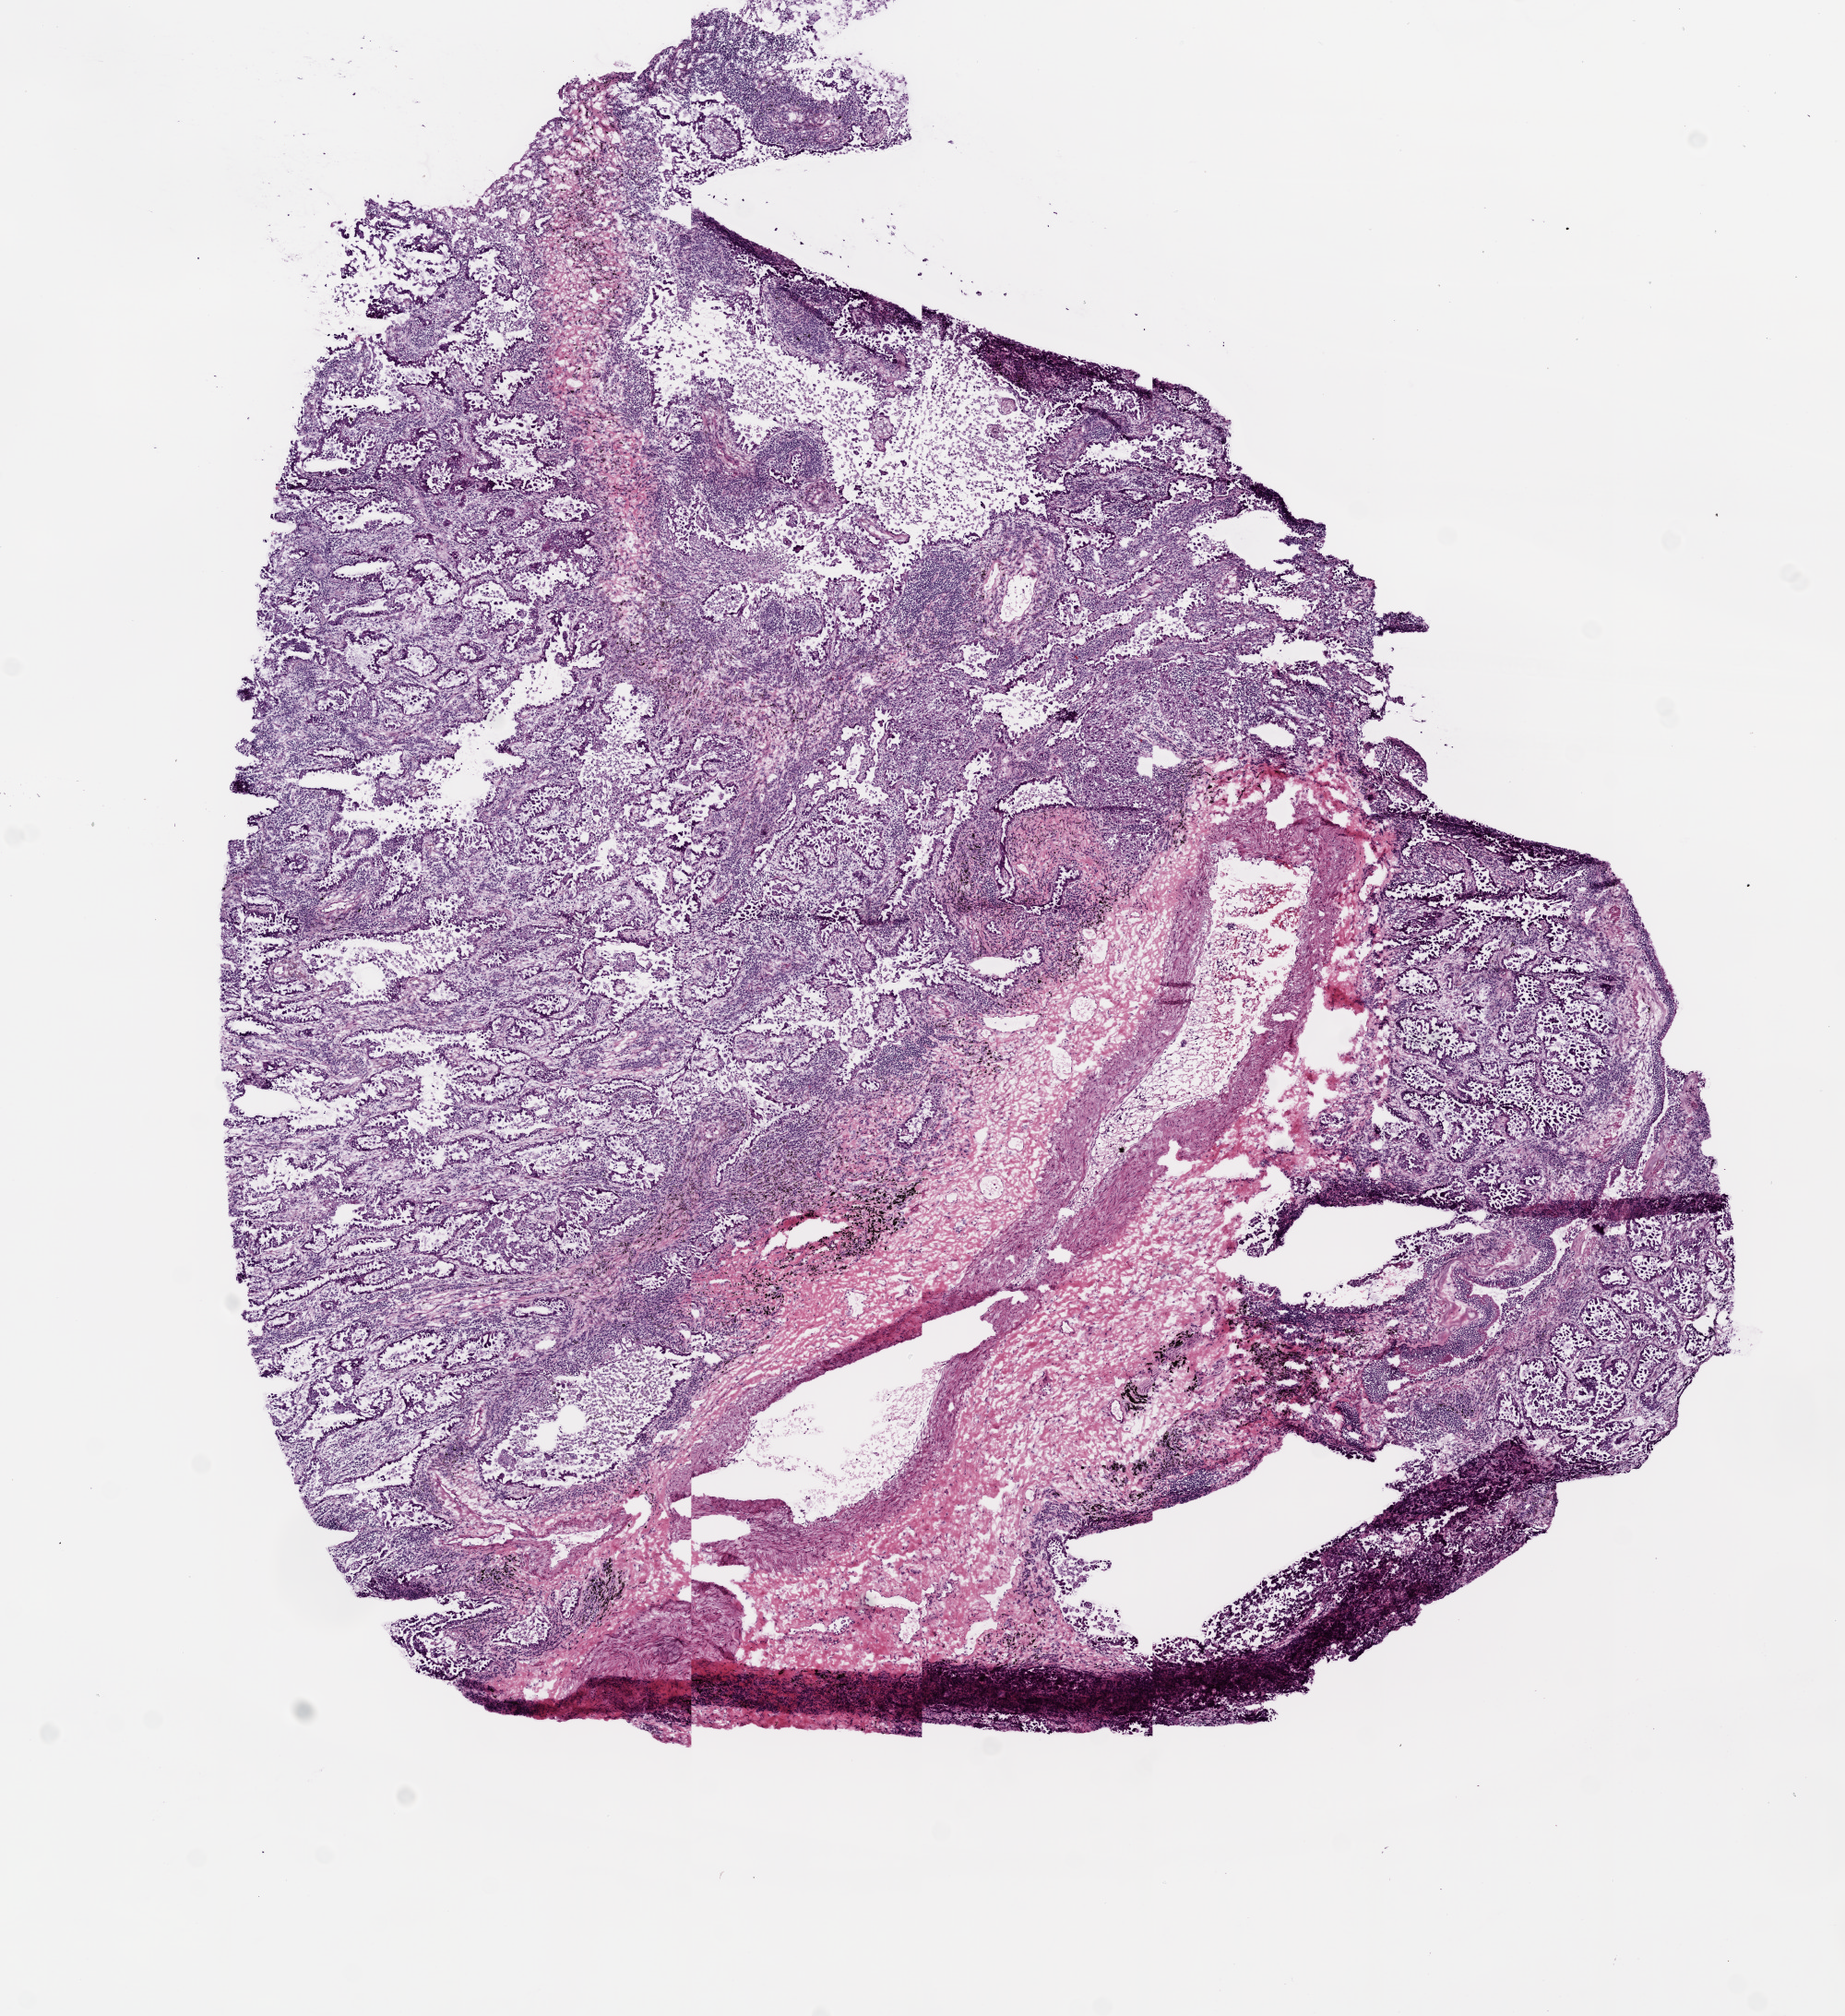
Whole-slide histology image, H&E-stained — a low-resolution overview of the entire scanned area, about 8.0 x 8.8 mm (acquisition: 20x scan), frozen section, sample: primary tumour, lung. Male patient; age at initial diagnosis 62 years. Pathologist review of this section (percent, as recorded): tumour cells 65%, tumour nuclei 60%, normal cells 10%, stromal cells 25%, necrosis 0%. Inflammatory infiltration, as recorded: lymphocyte infiltration 20%, monocyte infiltration 10%.
TNM: T2 N0 M0. AJCC pathologic stage: IB. Pathologic diagnosis: Adenocarcinoma with mixed subtypes (upper lobe, lung).